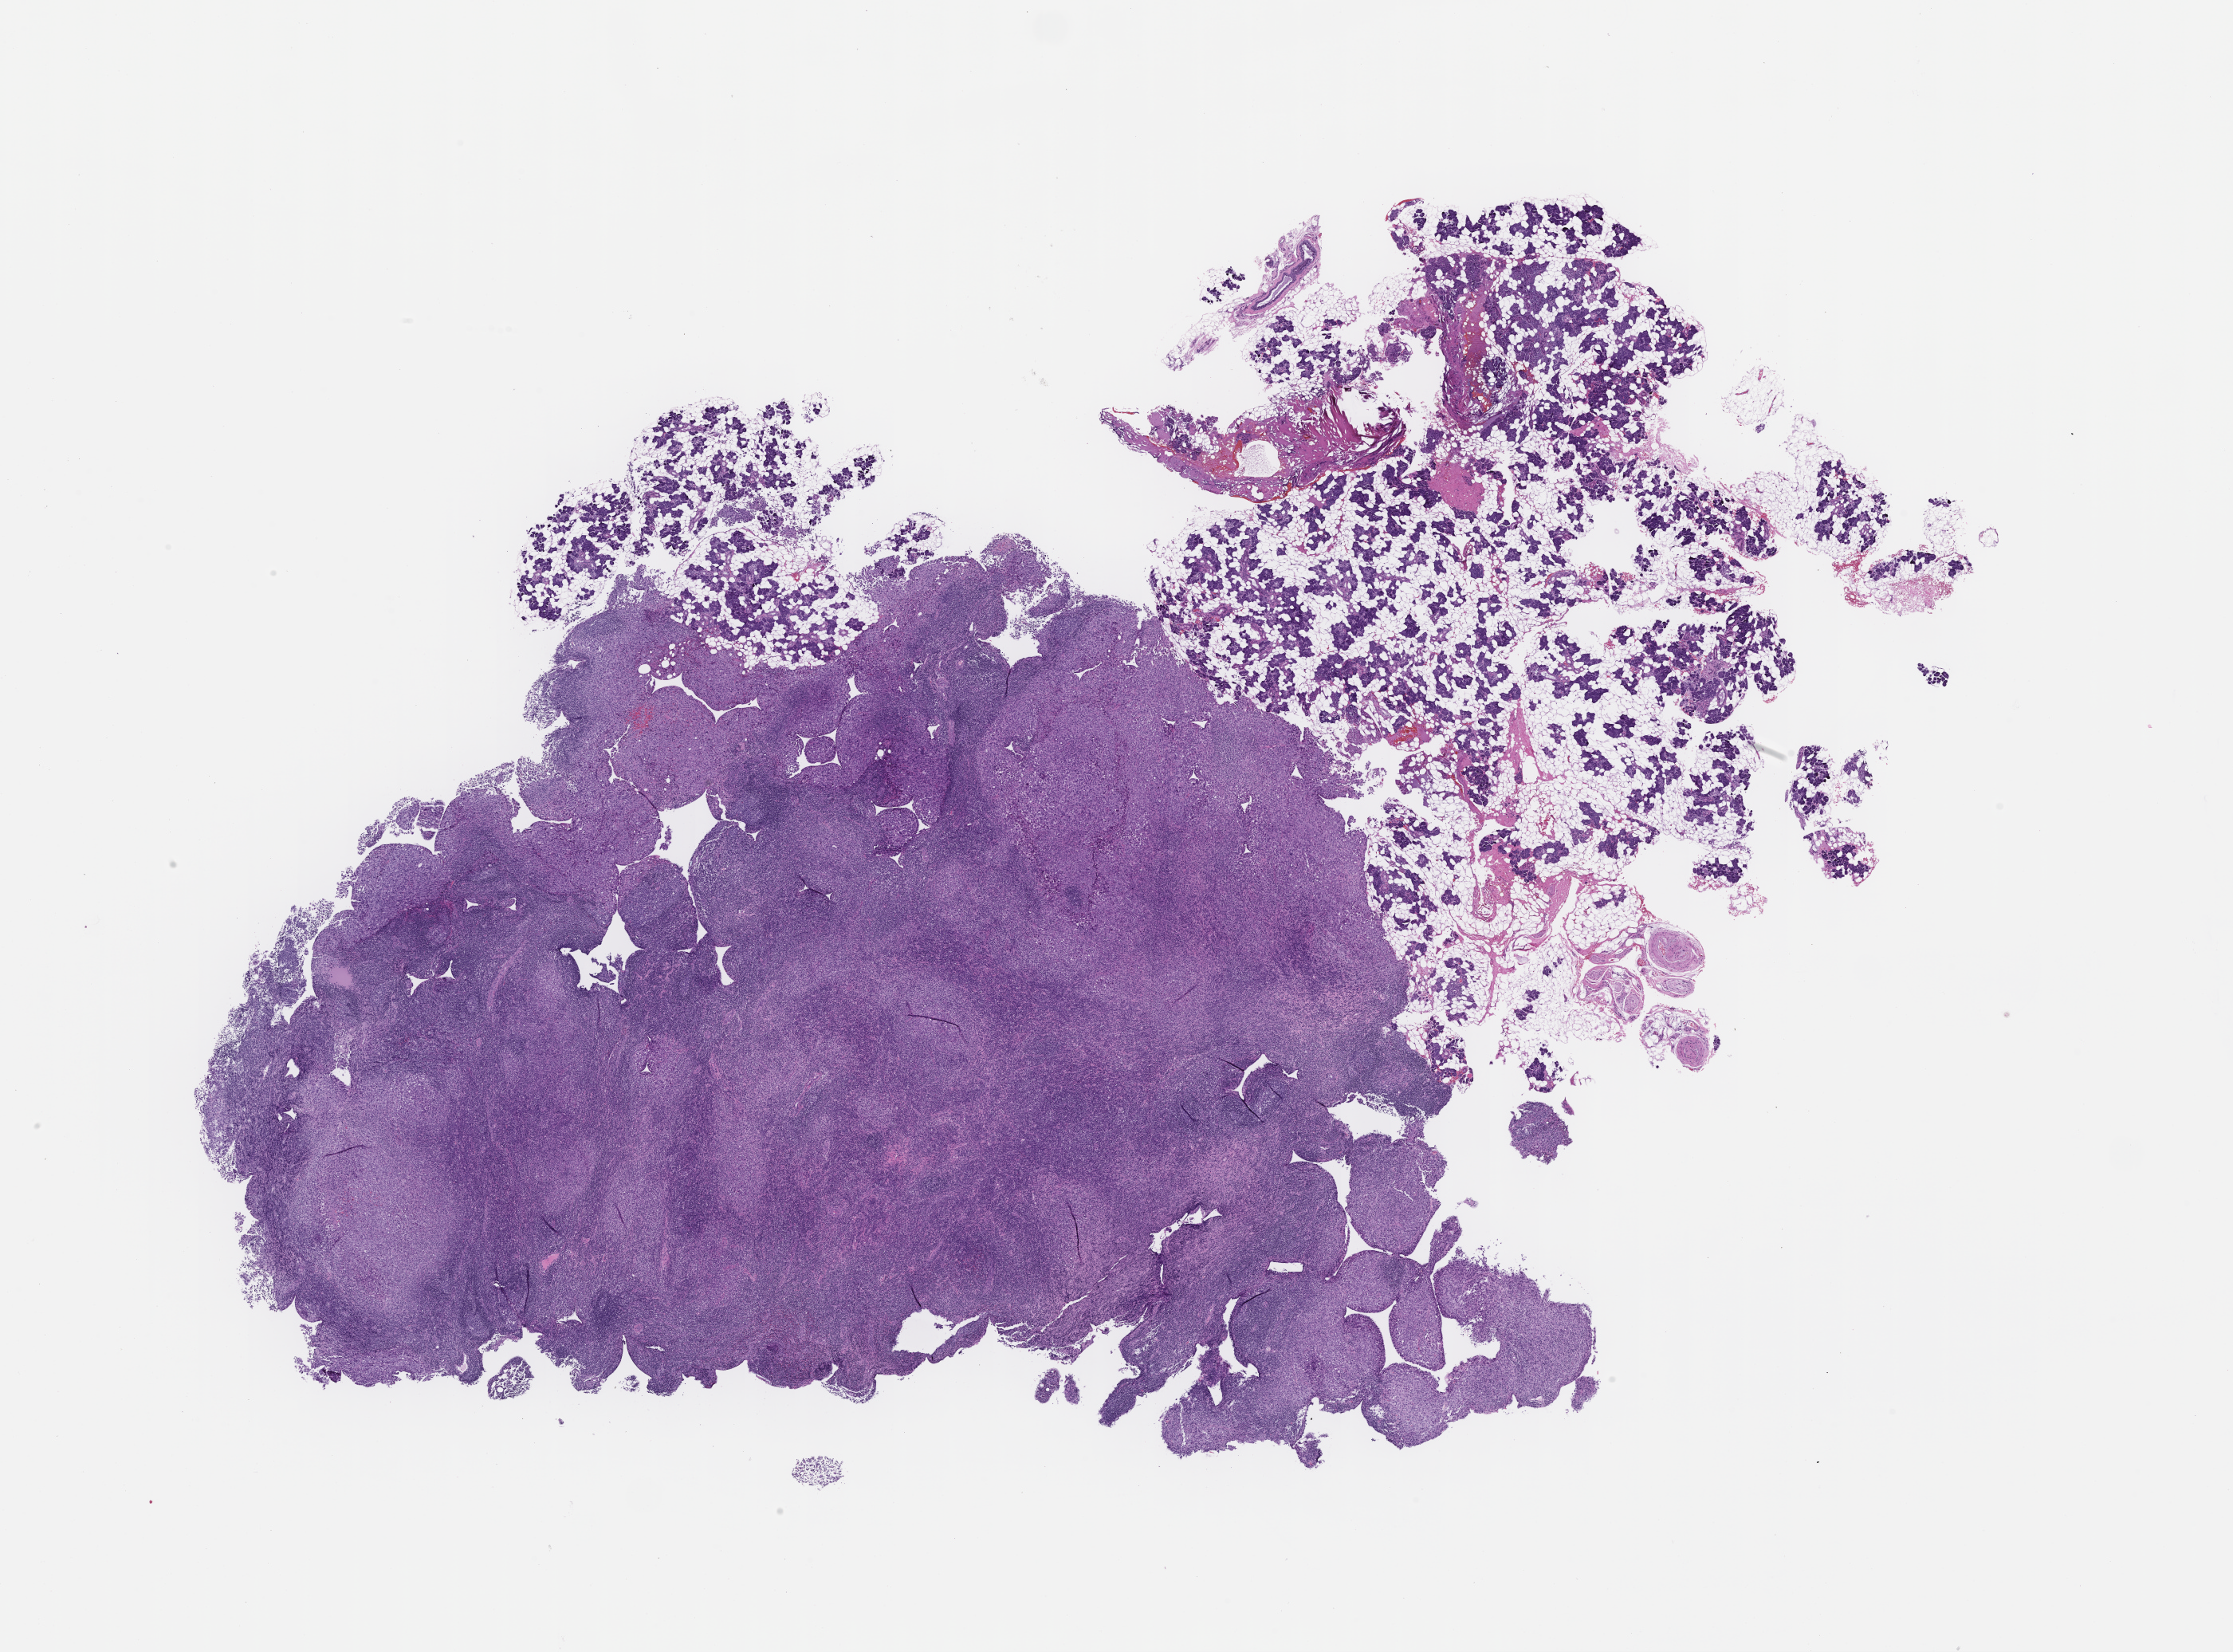
Digitized haematoxylin and eosin-stained section — whole scanned area (about 22.6 x 16.7 mm) shown as a low-resolution overview; formalin-fixed, paraffin-embedded (FFPE) tissue; specimen time point: collected on treatment. Patient: male.
* this section: metastasis (sampled organ not recorded)
* primary diagnosis of the patient: Melanoma